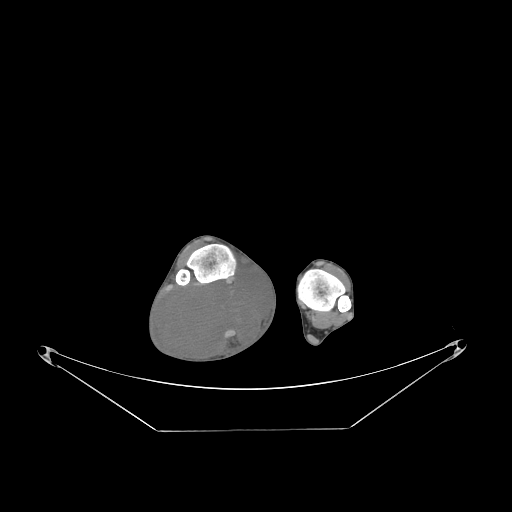
CT of an extremity soft-tissue mass (from a PET/CT study), one axial slice; position 53 of 267 along the scan axis; reconstruction kernel STANDARD; soft-tissue window (W 400 / L 40 HU); 3.75 mm slice thickness; 512 × 512 image matrix, field of view 500 × 500 mm. Male patient. Case-level facts recorded for this patient, not image findings: histological type: liposarcoma - round cell; grade: high; site of the primary tumour: right calf.
Structures marked on this image (expert contour drawn on MRI and transferred to this co-registered scan by the dataset authors):
- gross tumour volume (mass): bounding box (x1, y1, x2, y2) in pixels: (160, 272, 270, 362)